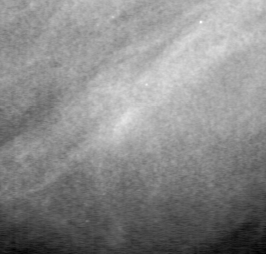
Cropped region of a digitized screen-film mammogram centred on a radiologist-marked abnormality, left breast, MLO view, BI-RADS breast density category 3 (scale 1–4).
Marked abnormality: mass, shape lobulated, margins obscured; BI-RADS assessment category 4; subtlety rating 3 on a 1 (subtle) to 5 (obvious) scale; pathology (as recorded): benign.